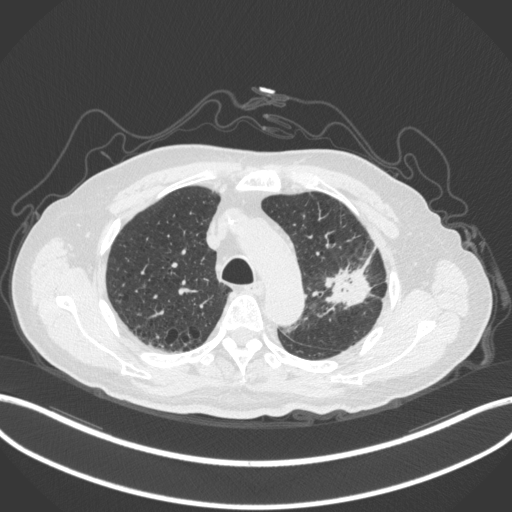
Chest CT, one axial slice; position 221 of 331 along the scan axis; reconstruction kernel B31f; 120 kVp; lung window (W 1500 / L -600 HU); 1 mm slice thickness; 512 × 512 image matrix, field of view 400 × 400 mm. Male patient, age 79 years. Case-level facts recorded for this patient, not image findings: clinical TNM (as recorded): T2a N1 M1; histopathological grade: G3.
Outlined on this slice (rectangle marked by the reading radiologist):
- lung tumour (recorded histology: adenocarcinoma): box from (x=319, y=262) to (x=372, y=311) px